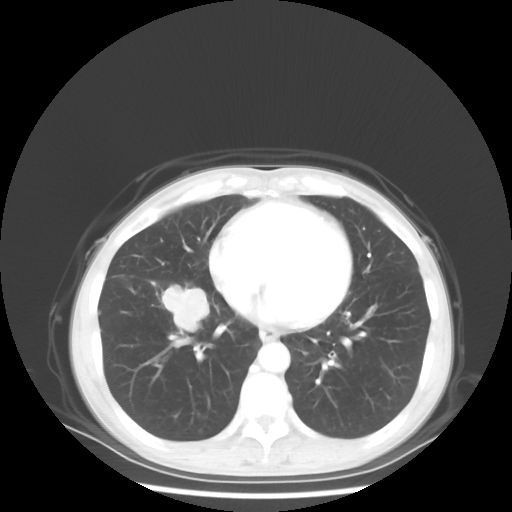
Chest CT, one axial slice; position 20 of 56 along the scan axis; reconstruction kernel STANDARD; 80 kVp; lung window (W 1500 / L -600 HU); 5 mm slice thickness; 512 × 512 image matrix, field of view 360 × 360 mm. Female patient, age 57 years. From the clinical record (not read from this slice): clinical TNM (as recorded): T1c N3 M1a; histopathological grade: G3.
Annotated regions visible in this slice (bounding box drawn by a radiologist):
- lung tumour (recorded histology: adenocarcinoma): bounding box [x1, y1, x2, y2] px = [159, 281, 213, 334]